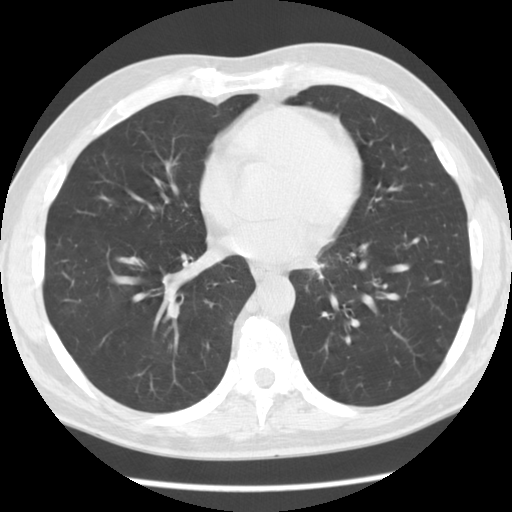
Chest CT (low-dose screening protocol), one axial image. First (baseline) screen. Lung window (W 1500 / L -600 HU). 2.5 mm slice thickness. Slice 69 of 112 in the series. 512 × 512 image matrix, field of view 340 × 340 mm. Male, age 55 years at enrolment.
Expert reader's lesion annotation, bounding box <286,235,344,290> (left, top, right, bottom; pixels). No non-calcified nodule or mass ≥4 mm was recorded by the screening reader at this exam. Official screen result: negative screen, minor abnormalities not suspicious for lung cancer. Participant outcome: lung cancer diagnosed 223 days after this screen — squamous cell carcinoma, NOS, left lower lobe, moderately differentiated (G2), stage IV (AJCC 6th edition), 51 mm at pathology.